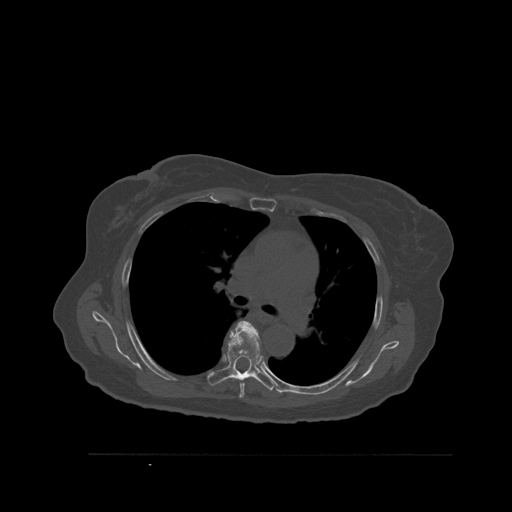
CT including the spine, one axial slice; position 385 of 527 along the scan axis; bone window (W 1800 / L 400 HU); 512 × 512 image matrix, field of view 470 × 470 mm. Patient: female, 73 years. From the clinical record (not read from this slice): primary cancer: breast; vertebrae with lytic lesions (as recorded): L2.
Outlined on this slice (semi-automatically segmented with operator editing):
- T5 vertebra: bounding box <238,331,259,399> (left, top, right, bottom; pixels)
- T6 vertebra: <207,321,276,391>